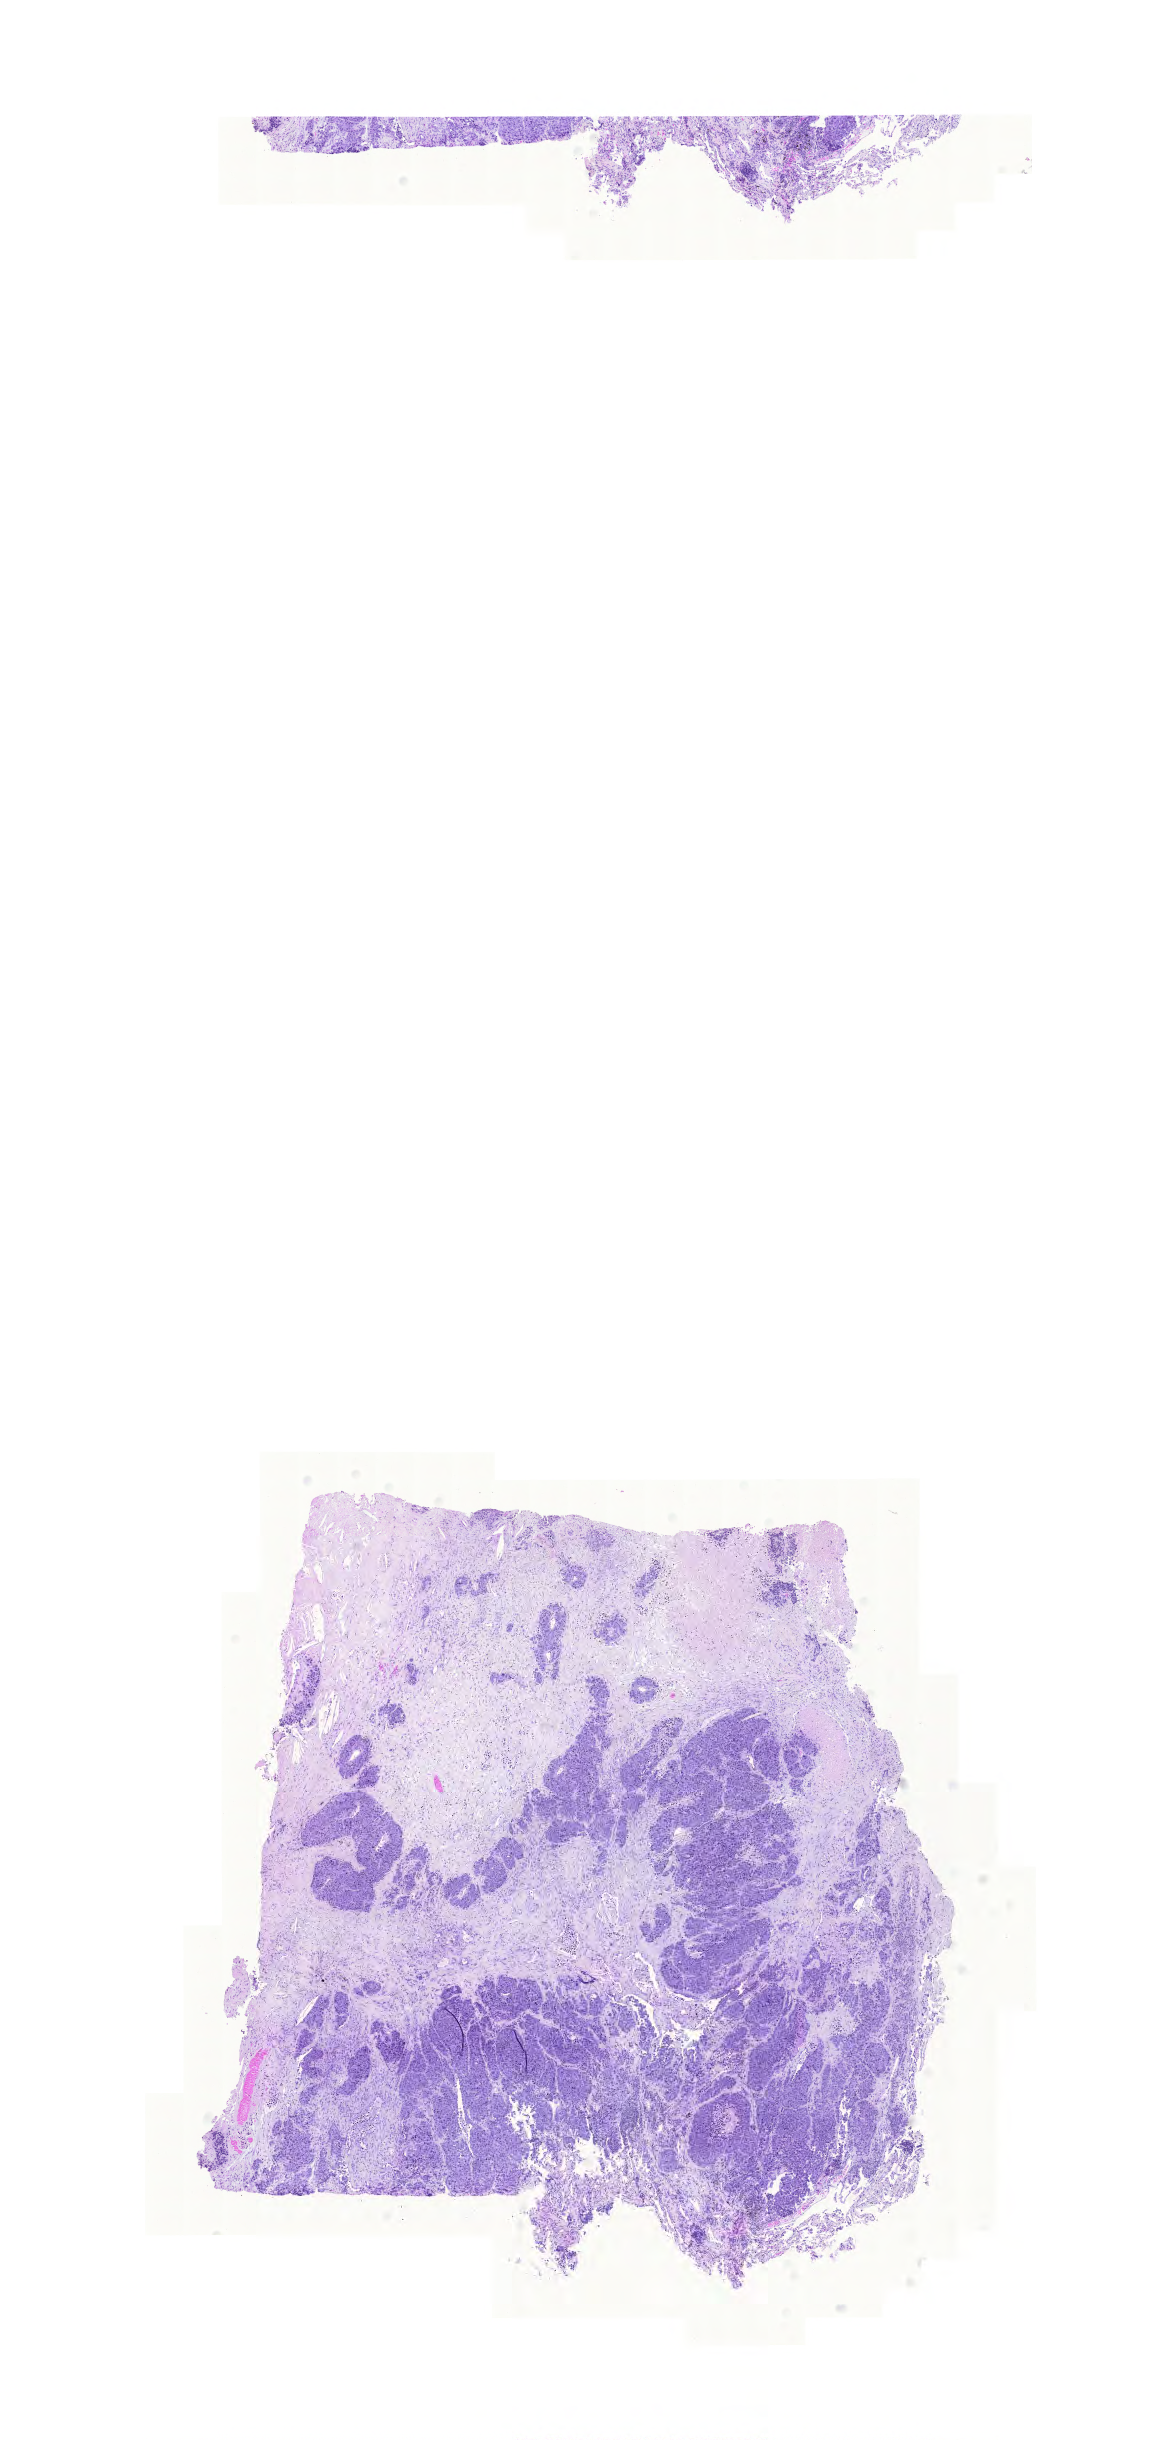
Digitized H&E-stained tissue section (whole slide), shown as a low-resolution overview of the whole scanned area (about 8.6 x 18.2 mm, from a 20x scan). Formalin-fixed paraffin-embedded (FFPE) diagnostic section. Lung, primary tumour sample. Patient: male, age at initial diagnosis 81 years.
Laterality: left. Histologic diagnosis: Adenocarcinoma, NOS. TNM: T2 N2 M0. AJCC pathologic stage: IIIA (6th edition).